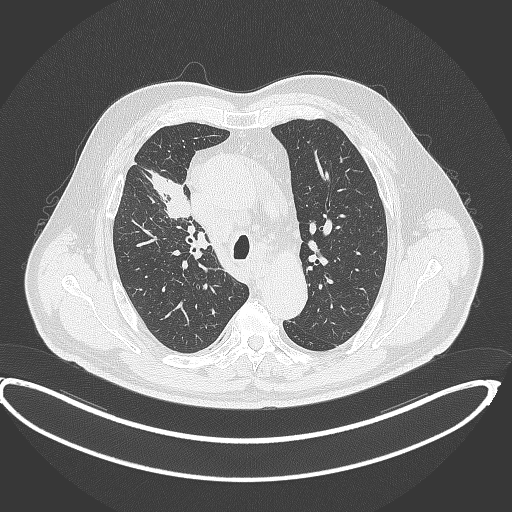
Chest CT, one axial slice. Position 286 of 390 along the scan axis. Reconstruction kernel B70f. 120 kVp. Lung window (W 1500 / L -600 HU). 1 mm slice thickness. 512 × 512 image matrix. Patient: male, 62 years. From the clinical record (not read from this slice): clinical TNM (as recorded): T1c N3 M1c.
Annotated regions visible in this slice (rectangle marked by the reading radiologist):
- lung tumour (recorded histology: adenocarcinoma): bounding box <148,166,193,222> (left, top, right, bottom; pixels)